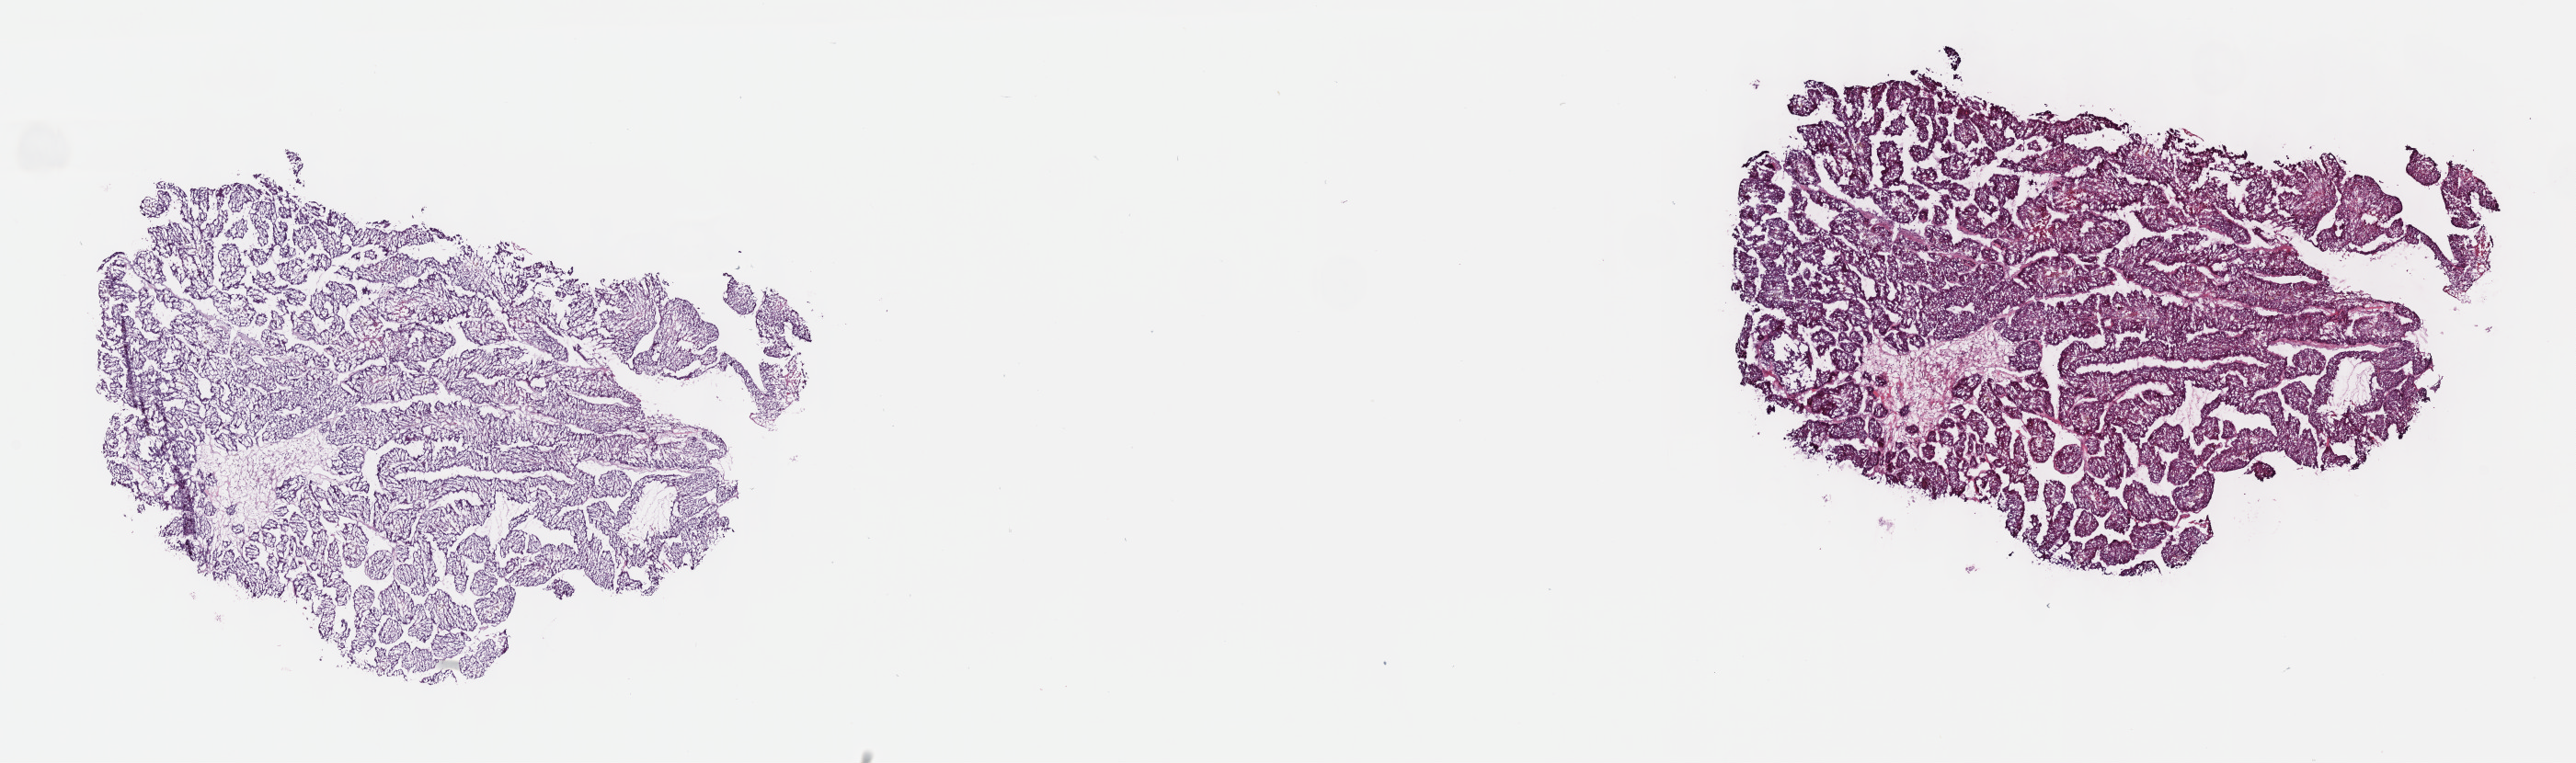
Digitized Hematoxylin and eosin (H&E) stained tissue section (whole slide) — shown as a low-resolution overview of the whole scanned area (about 22.7 x 6.7 mm); frozen section from the top of the tissue portion; sample: primary tumour, liver. Patient: male, age at initial diagnosis 61 years. Composition of this section per pathologist review: tumour cells 100%, tumour nuclei 80%.
Pathologic diagnosis: Hepatocellular carcinoma, NOS.